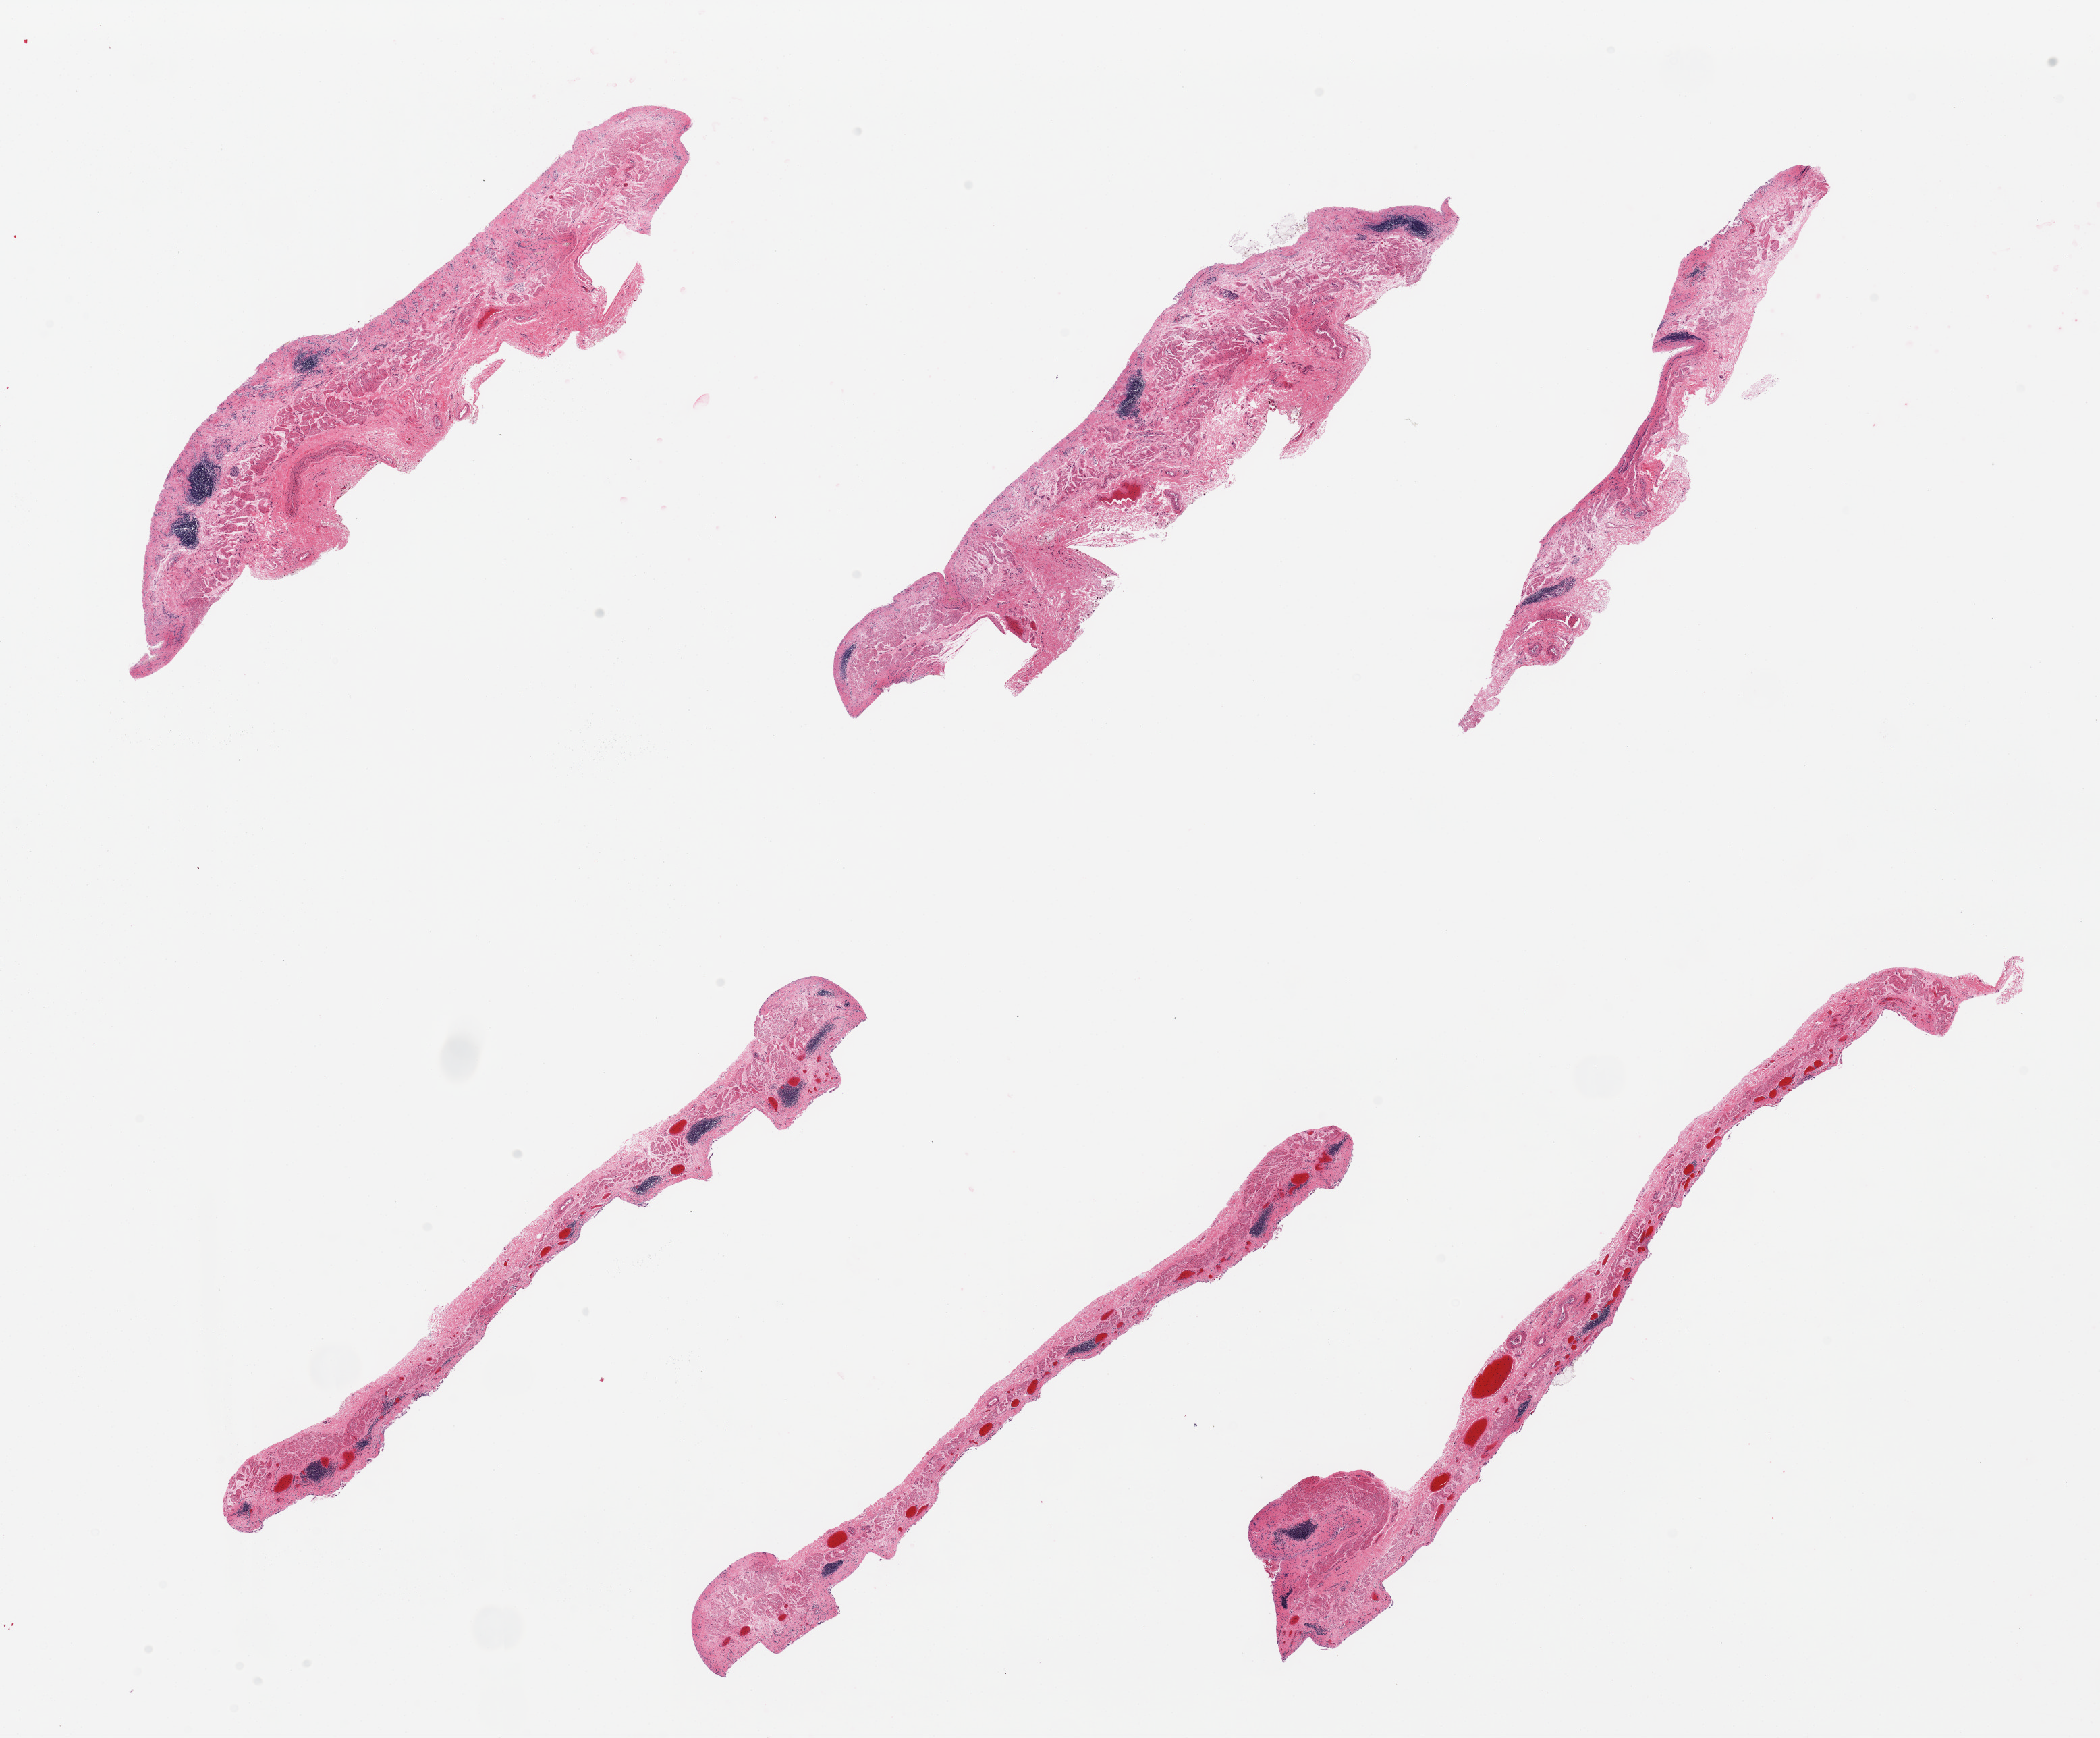
Whole-slide image, haematoxylin and eosin stain, low-resolution overview of the scanned area, about 24.6 x 20.4 mm (from a 20x scan). PAXgene-fixed paraffin-embedded (PFPE) section. Target tissue: esophageal mucous membrane. Tissue donor sample. Male donor.
Review note (as recorded): 6 pieces, markedly autolyzed, mucosa sloughed, submucosal lymphoid aggregates present.